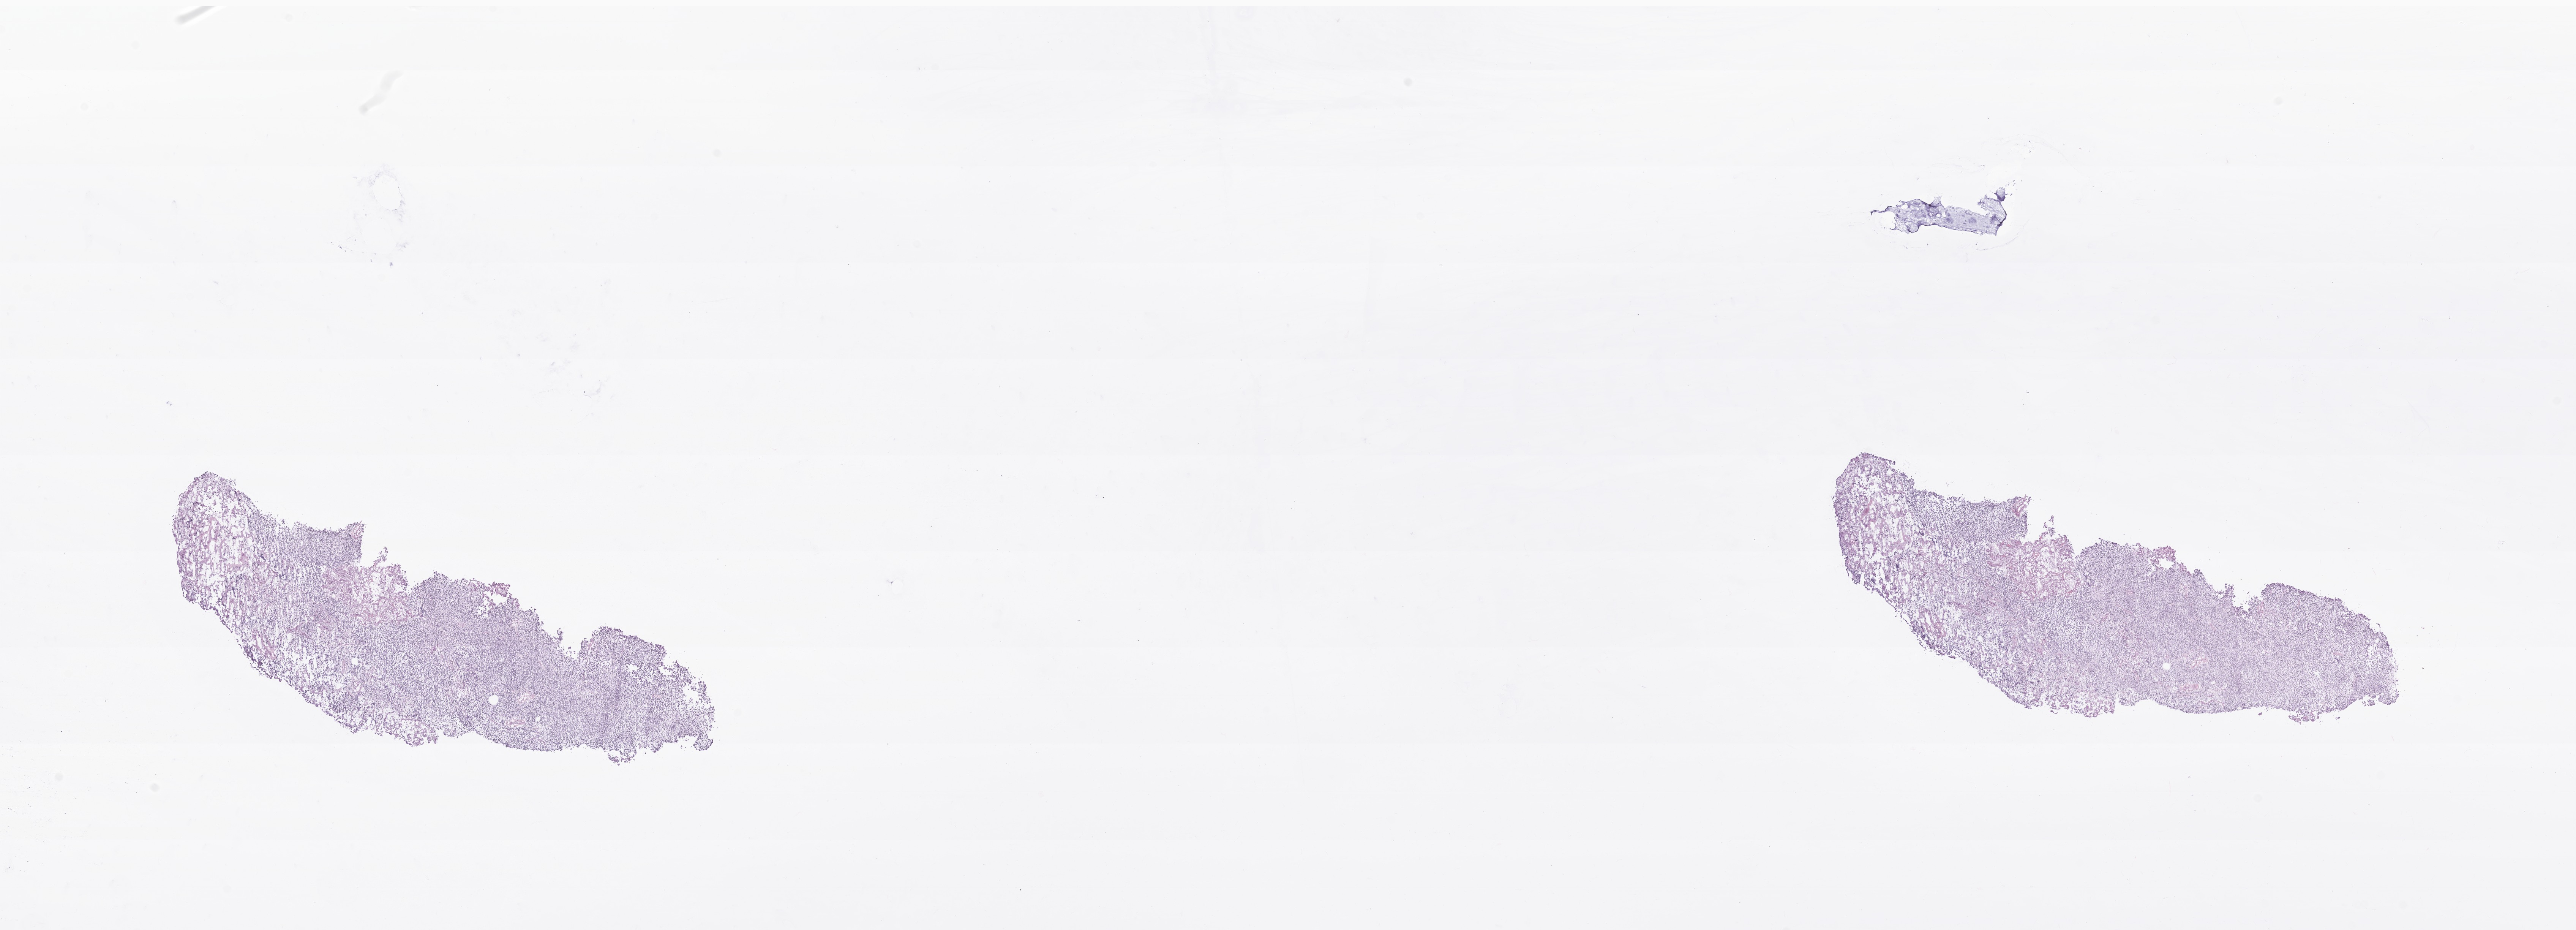
Whole-slide image, H&E stain of tumor tissue from the cerebral ventricle, shown as a low-resolution overview of the whole scanned area (about 28.5 x 10.3 mm); cryosection (OCT / tissue freezing medium). Female patient, age 90 months (7 years 6 months).
Diagnosis: Medulloblastoma, NOS.